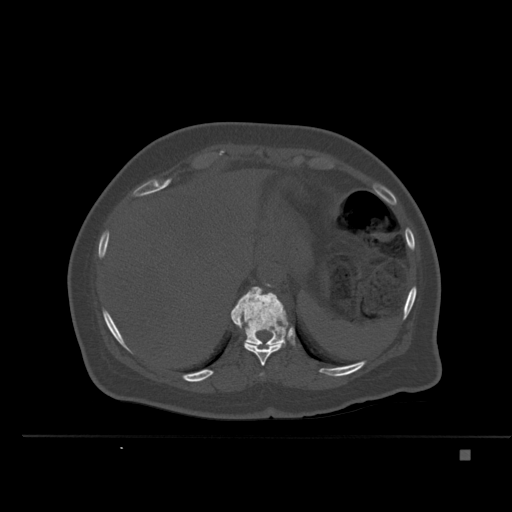
CT including the spine, one axial slice; slice 277 of 477 in the series (ordered by position); bone window (W 1800 / L 400 HU); 512 × 512 image matrix, field of view 422 × 422 mm. Female patient, age 74 years. Case-level facts recorded for this patient, not image findings: primary cancer: colon.
Structures marked on this image (semi-automatic segmentation, software-assisted and operator-edited):
- T10 vertebra: bounding box [x1, y1, x2, y2] px = [237, 324, 284, 366]
- T11 vertebra: [230, 286, 288, 346]
- T9 vertebra: [260, 373, 264, 376]